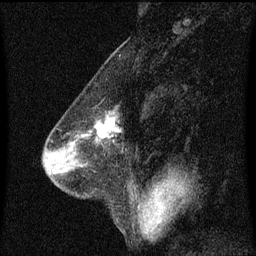
Breast MRI (dynamic contrast-enhanced), one sagittal slice; slice 30 of 60 in the series (ordered by position); dynamic contrast-enhanced series, image 2 of 3 at this slice position (ordered by acquisition); 1.5 T; TE 4.2 ms, TR 8.4 ms; 2 mm slice thickness; 256 × 256 image matrix, field of view 200 × 200 mm. Patient: female, 58 years.
Structures marked on this image (semi-automatic segmentation, software-assisted and operator-edited):
- analysis volume of interest (the breast-tissue region the enhancement analysis was run in; not a lesion): bounding box (x1, y1, x2, y2) in pixels: (79, 110, 123, 143)
- tumour enhancement mask (voxels above the 70 % enhancement threshold inside the analysis volume of interest): (91, 118, 119, 139)